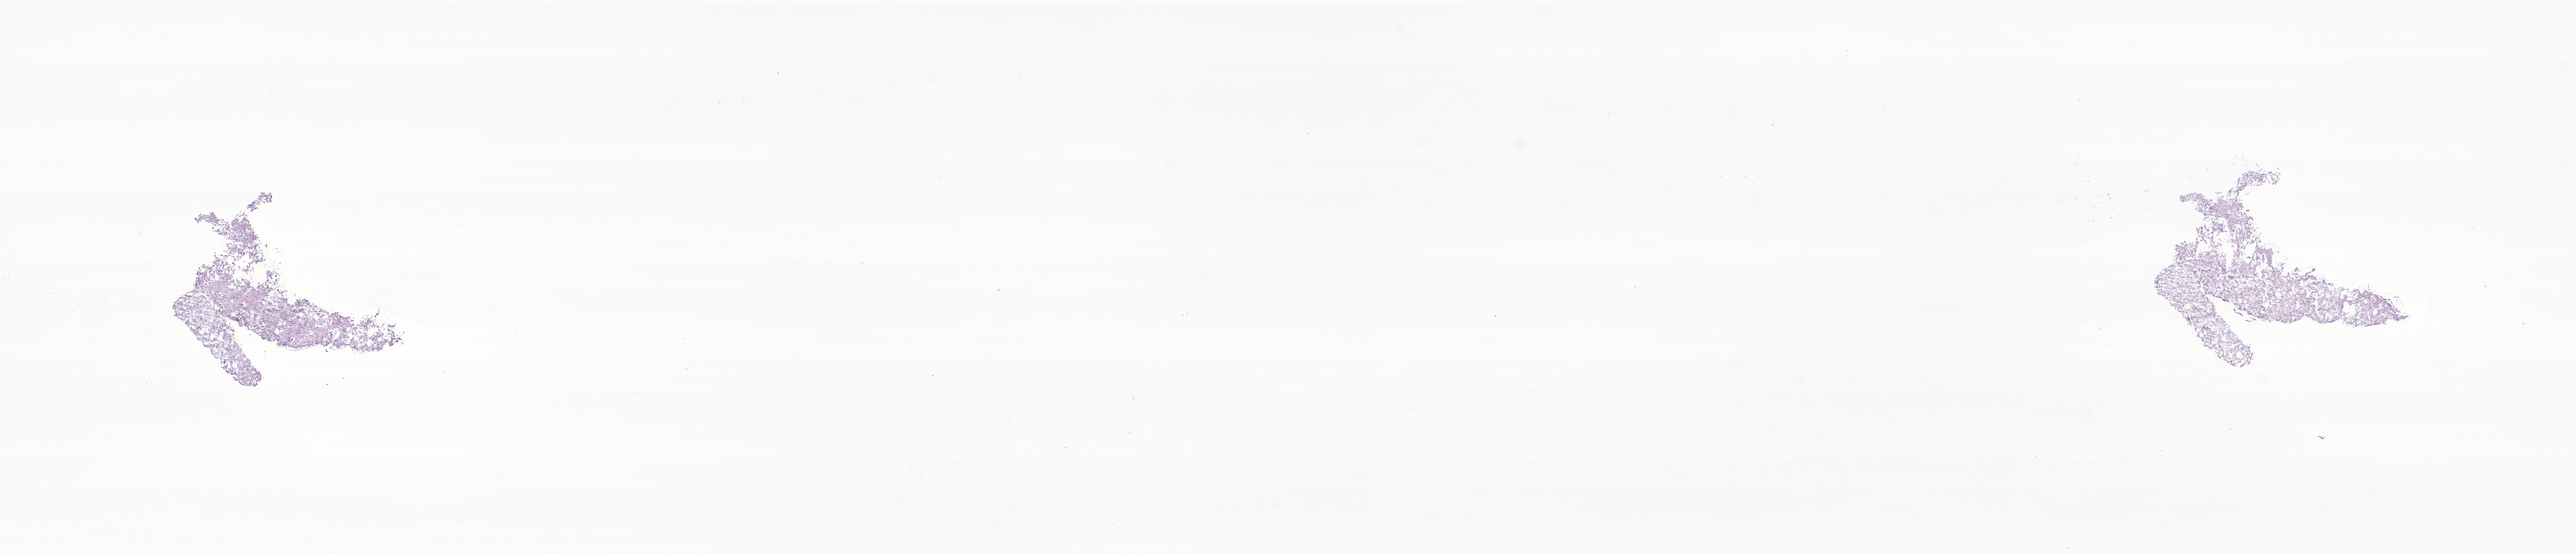
Hematoxylin and eosin (H&E) whole-slide image of tumor tissue from the brain, a low-resolution overview of the entire scanned area, about 27.6 x 5.9 mm; cryosection (OCT / tissue freezing medium). Patient: male, age 925 days (about 2.5 years).
• diagnosis (ICD-O-3 morphology term): Pilocytic astrocytoma